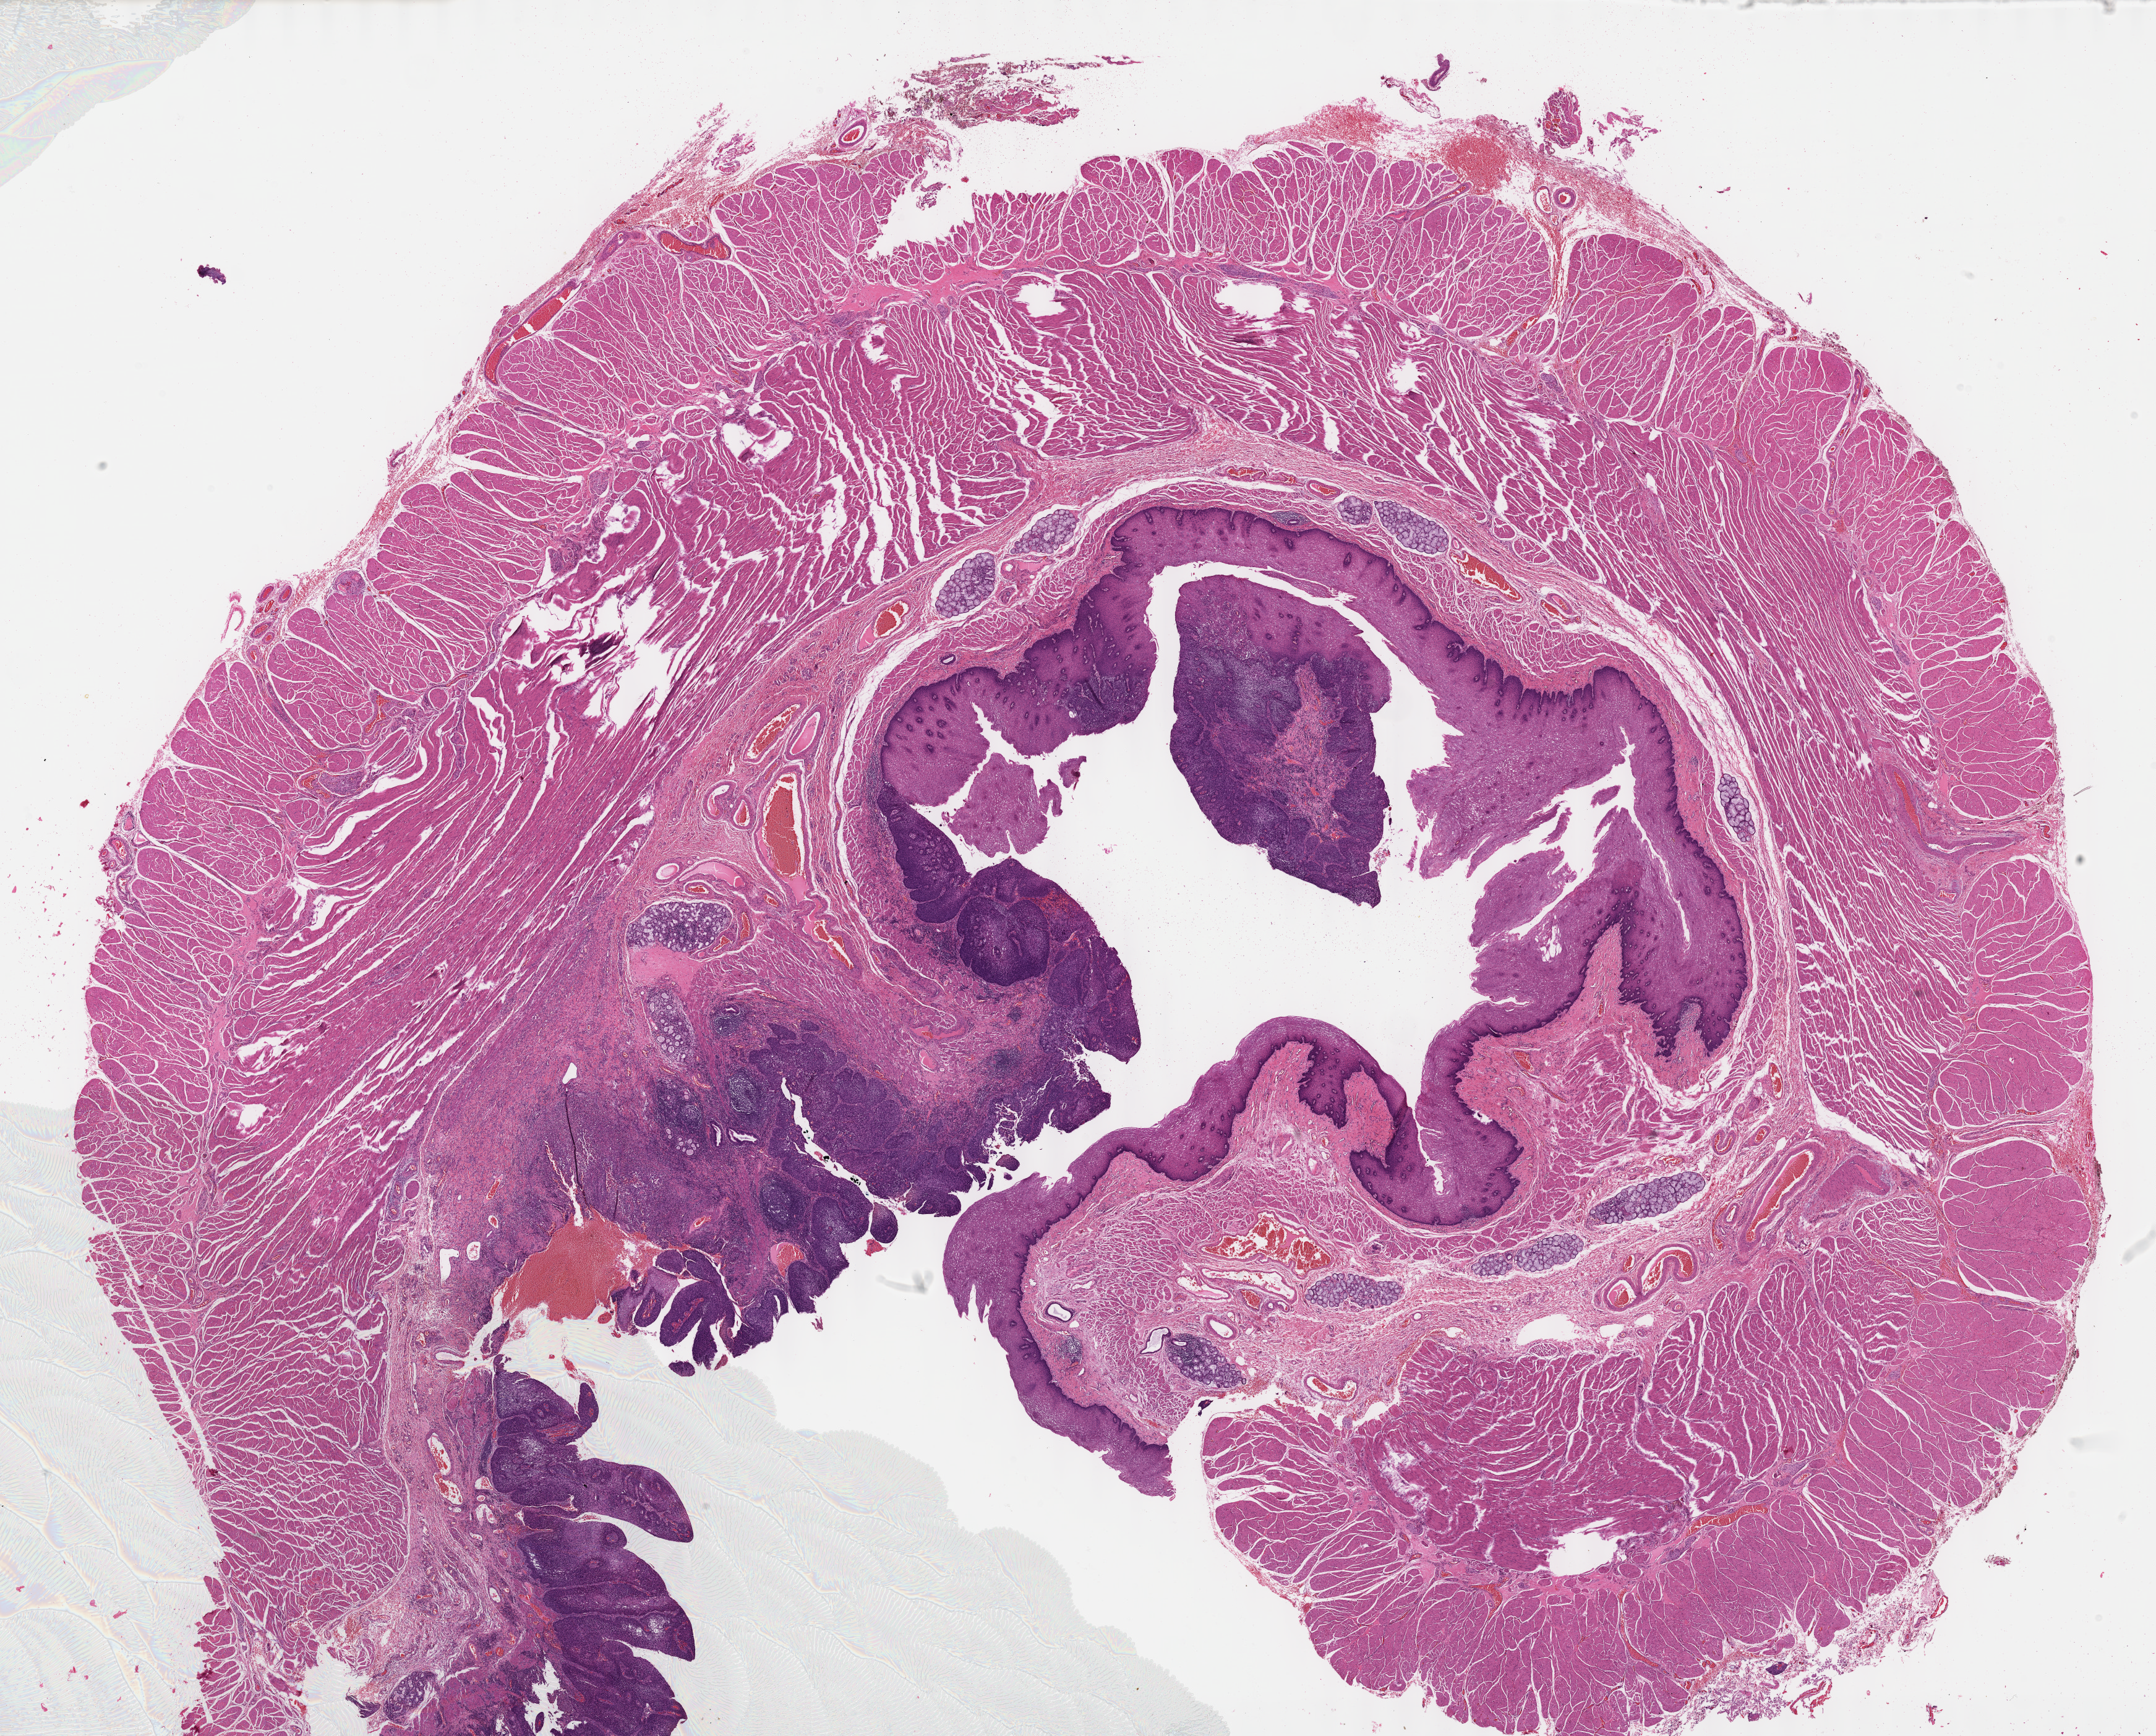
Hematoxylin and eosin (H&E) stained whole-slide image — shown as a low-resolution overview of the whole scanned area (about 28.2 x 22.7 mm); formalin-fixed paraffin-embedded (FFPE) diagnostic section; esophagus, primary tumour sample. Male patient; age at initial diagnosis 49 years. Histologic grade: G1 (well differentiated).
• lymph nodes positive (case pathology): 1 of 10 examined
• AJCC pathologic stage: IIB (7th edition)
• pathologic diagnosis: Squamous cell carcinoma, NOS (lower third of esophagus)